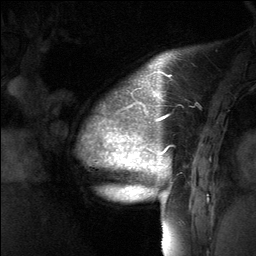
Breast MRI (dynamic contrast-enhanced), one sagittal slice. Position 13 of 64 along the scan axis. Dynamic contrast-enhanced study with each time point stored as its own series, time point 2 of 3 at this slice position (early post-contrast, ordered by acquisition time). 1.5 T. TE 4.8 ms, TR 27 ms. 2 mm slice thickness. 256 × 256 image matrix, field of view 200 × 200 mm. Patient: female, 39 years. Case-level facts recorded for this patient, not image findings: setting: breast cancer imaged before/during neoadjuvant chemotherapy; receptor status: HER2-positive.
Annotated regions visible in this slice (semi-automatically segmented with operator editing):
- analysis volume of interest (the breast-tissue region the enhancement analysis was run in; not a lesion): bounding box [x1, y1, x2, y2] px = [79, 69, 202, 224]
- tumour enhancement mask (voxels above the 90 % enhancement threshold inside the analysis volume of interest): [104, 75, 171, 191]